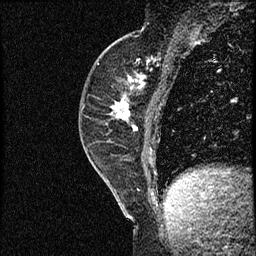
Breast MRI (dynamic contrast-enhanced), one sagittal slice. Slice 25 of 56 in the series (ordered by position). Dynamic contrast-enhanced study with each time point stored as its own series, time point 2 of 3 at this slice position (early post-contrast, ordered by acquisition time). 1.5 T. TE 4.2 ms, TR 17.3 ms. 256 × 256 image matrix, field of view 200 × 200 mm. Female patient. Case-level facts recorded for this patient, not image findings: setting: breast cancer imaged before/during neoadjuvant chemotherapy; receptor status: HER2-positive.
Structures marked on this image (semi-automatic segmentation, software-assisted and operator-edited):
- analysis volume of interest (the breast-tissue region the enhancement analysis was run in; not a lesion): bounding box (x1, y1, x2, y2) in pixels: (79, 50, 156, 155)
- tumour enhancement mask (voxels above the 100 % enhancement threshold inside the analysis volume of interest): (112, 76, 144, 130)